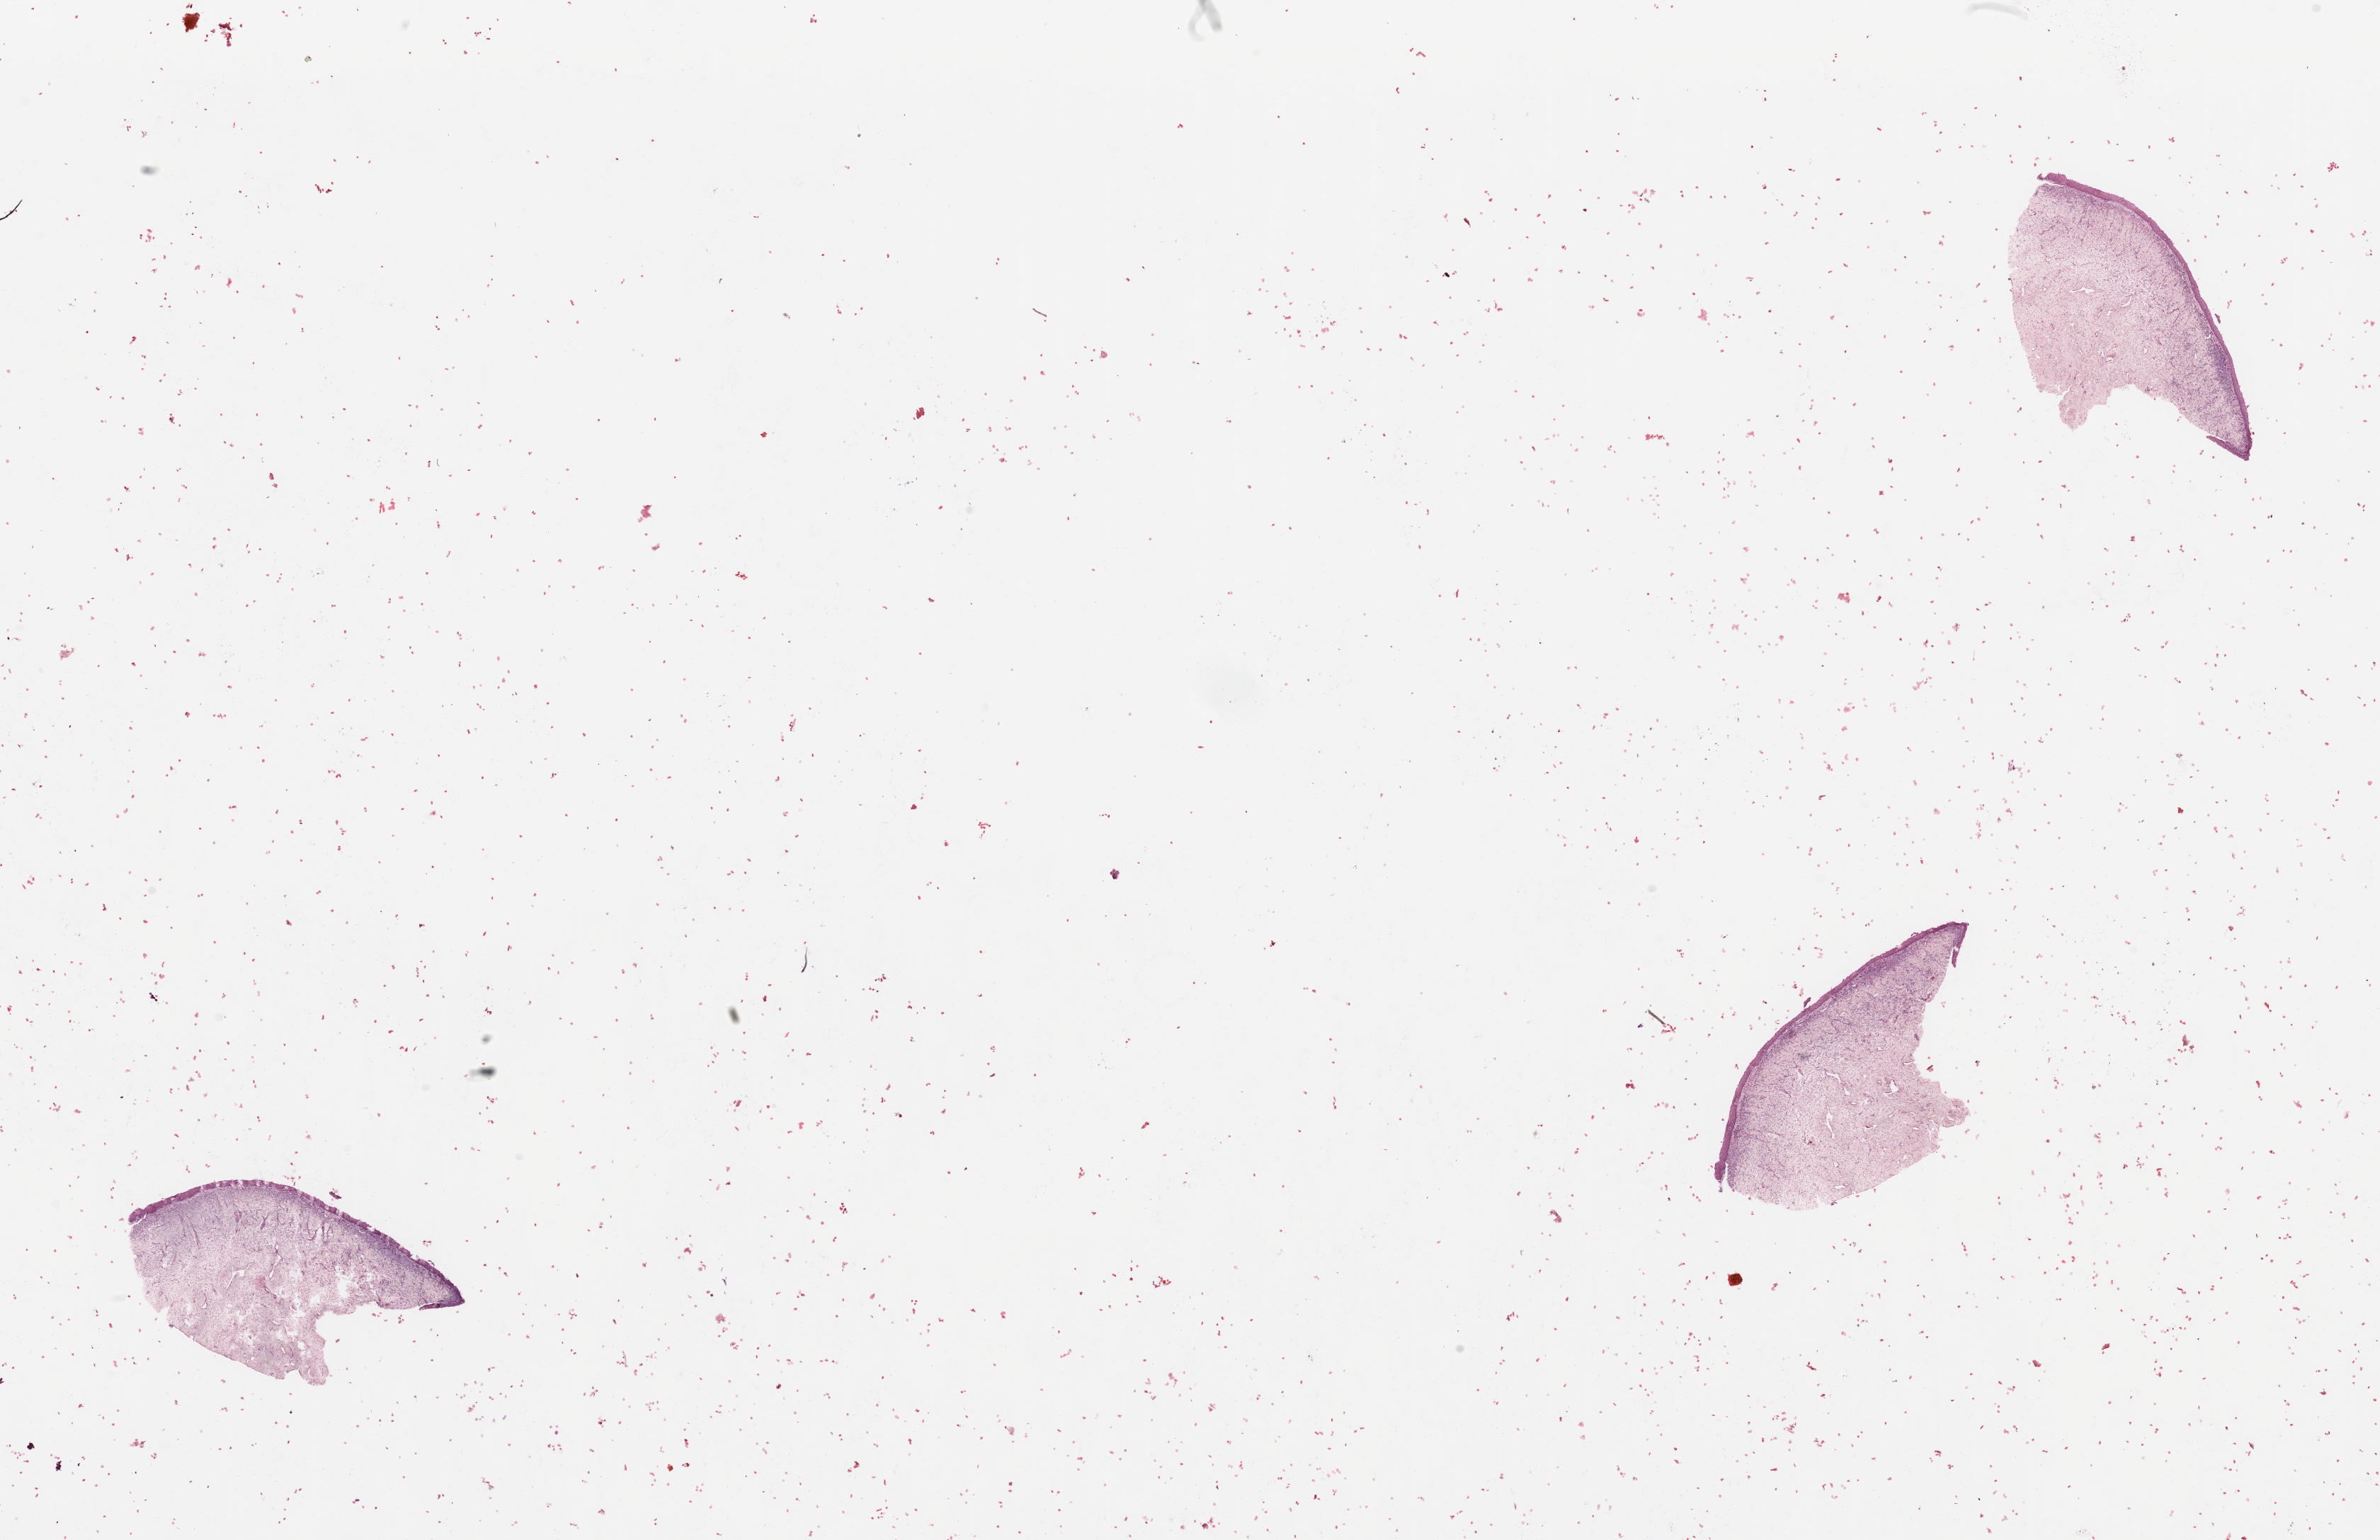
Digitized H&E-stained tissue section (whole slide) — shown as a low-resolution overview of the whole scanned area (about 26.6 x 17.2 mm). Normal (non-tumour) tissue sample, uterus. Female, 60 y/o.
• this section: normal (non-tumour) tissue from the same patient
• patient diagnosis: Endometrioid adenocarcinoma, NOS